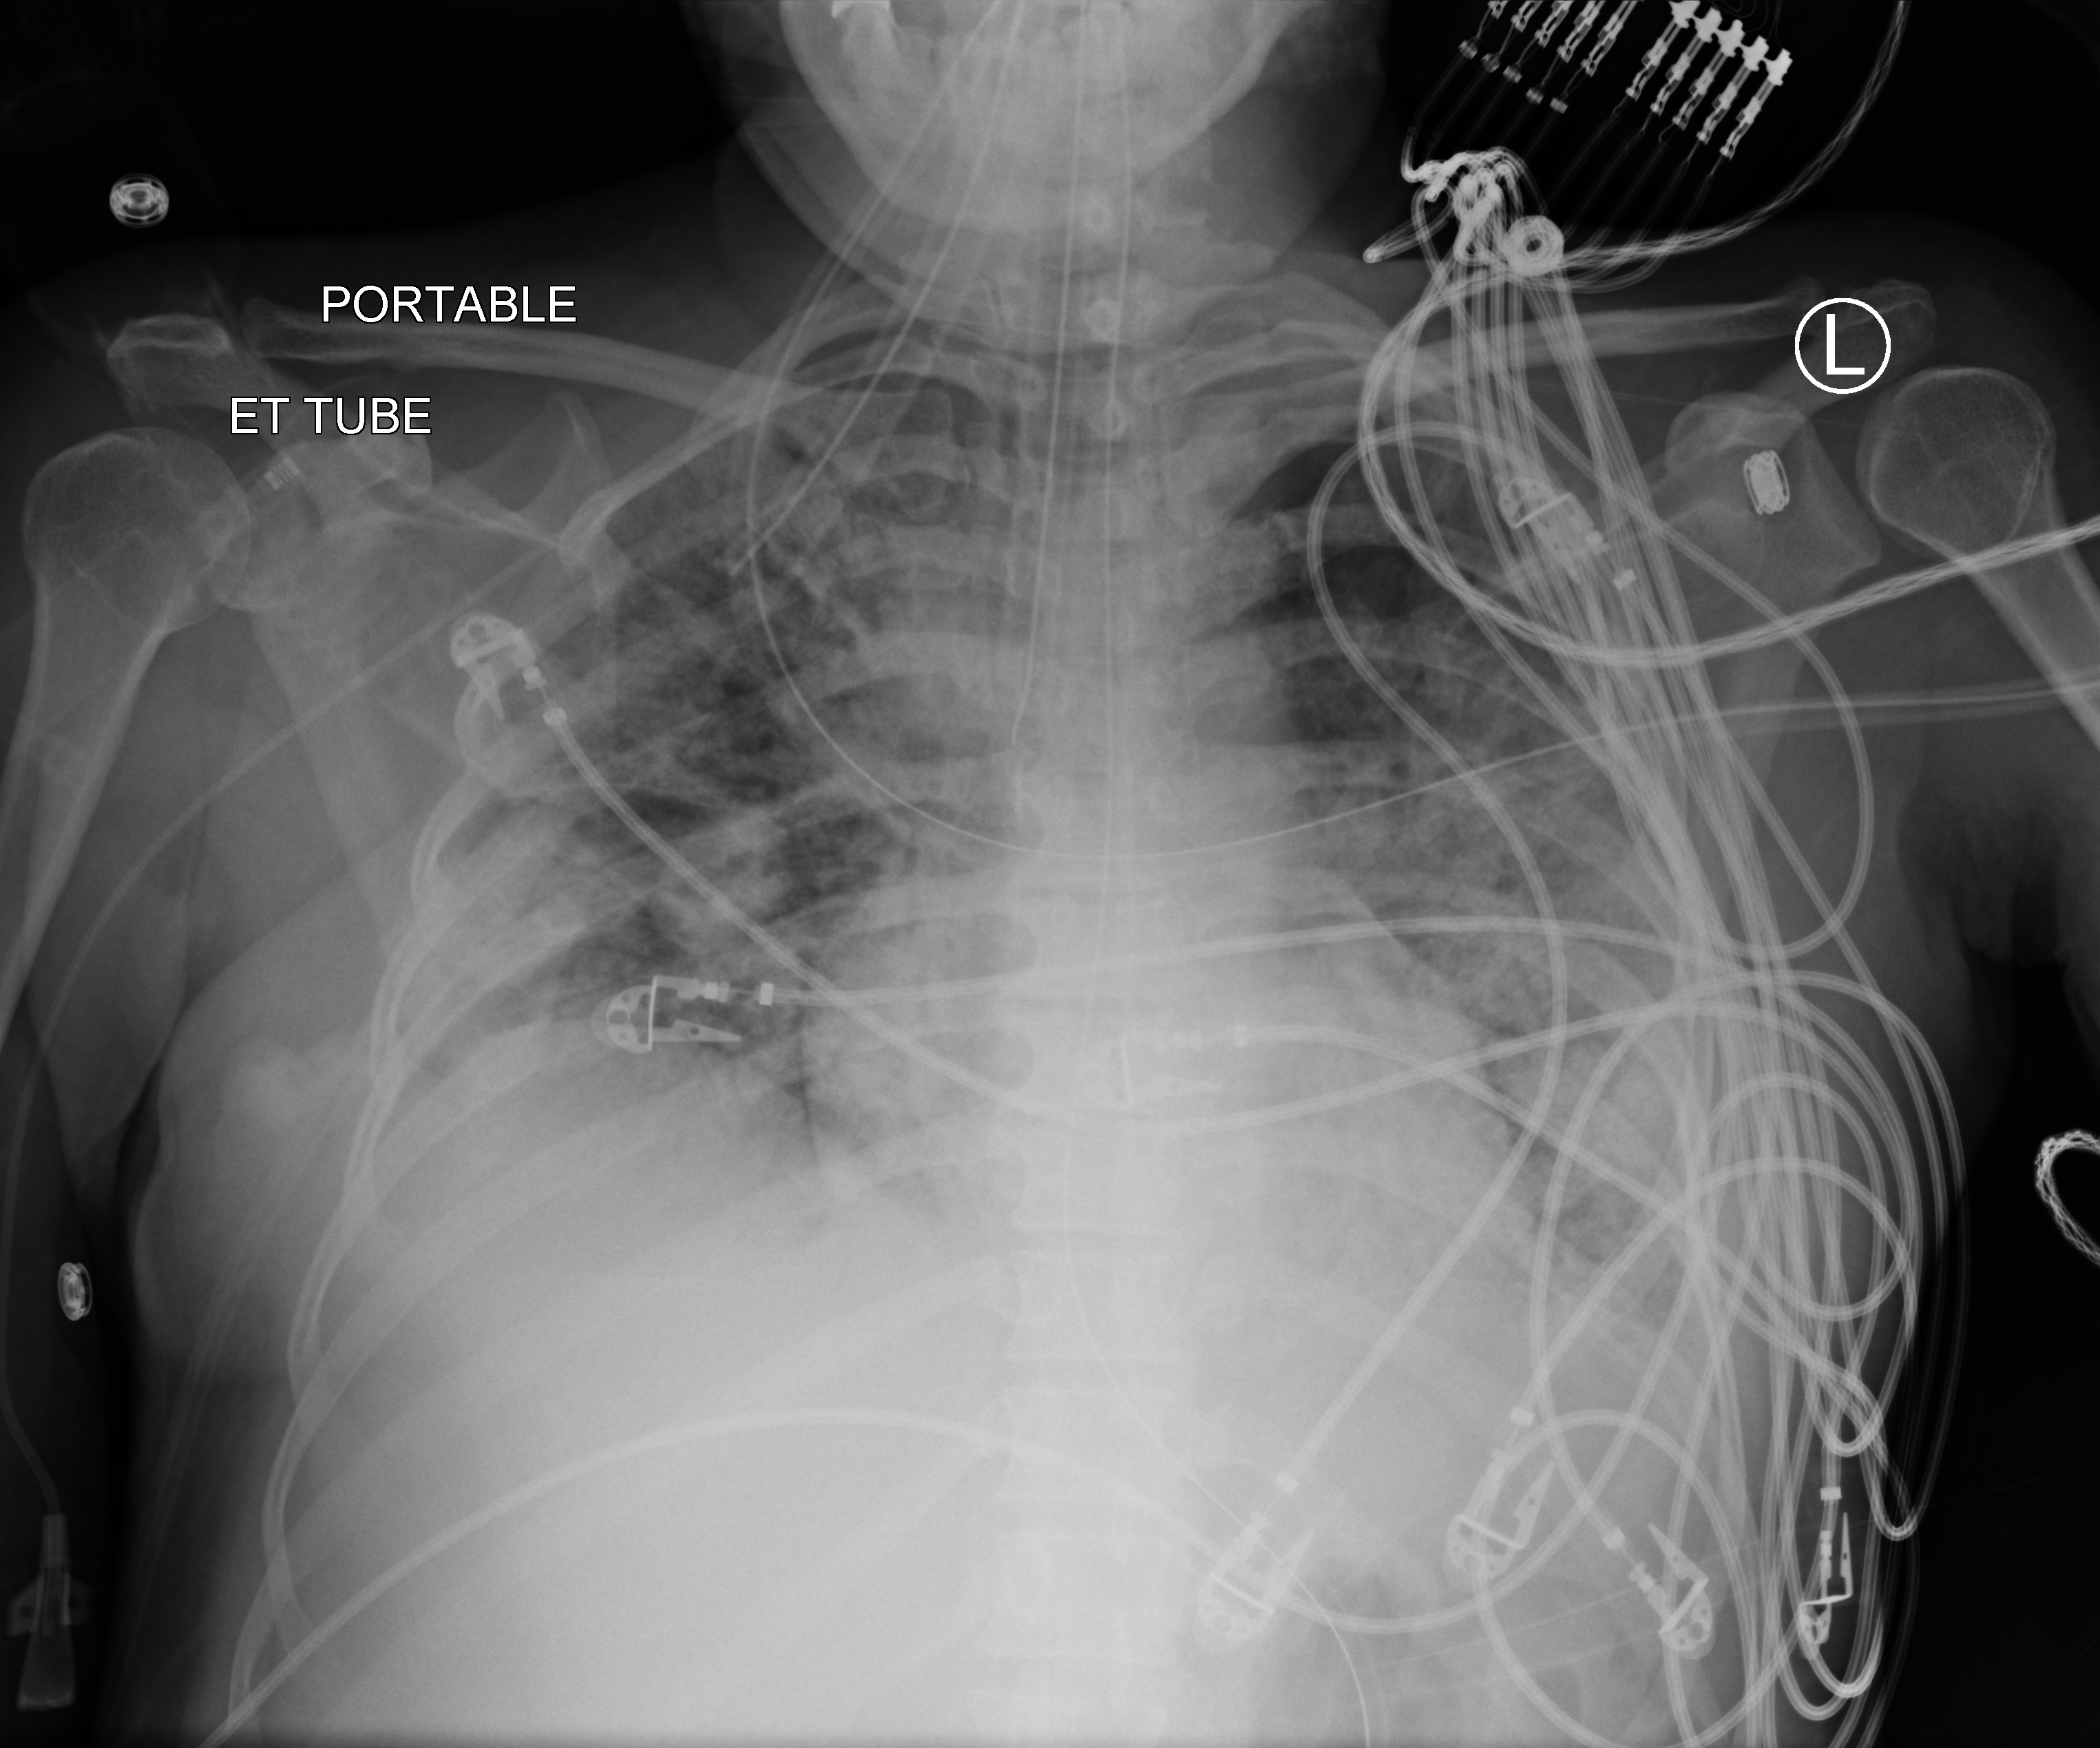
Portable chest radiograph, anteroposterior (AP) projection. Patient hospitalised with COVID-19; female, aged 18–59 years.
Hospital-stay facts (about this admission, not read from this image; timing relative to this image not recorded): COPD (admission record): no; length of hospital stay: 71 days; smoking status (admission record): former.